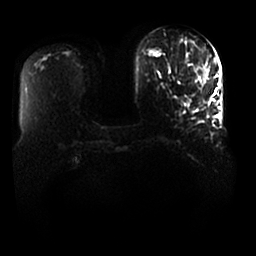
Breast MRI, one axial slice; slice 3 of 25 in the series (ordered by position); diffusion-weighted series; image 2 of 4 stored at this slice position (different b-values; order by instance number); 1.5 T; 256 × 256 image matrix, field of view 370 × 370 mm. Female patient.
Structures marked on this image (manually delineated by an expert):
- tumour on diffusion-weighted imaging: bounding box (x1, y1, x2, y2) in pixels: (203, 69, 206, 83)